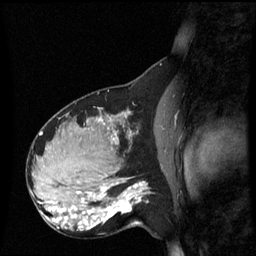
Breast MRI (dynamic contrast-enhanced), one sagittal slice. Position 34 of 60 along the scan axis. Dynamic contrast-enhanced series, image 2 of 3 at this slice position (ordered by acquisition). 1.5 T. TE 4.2 ms, TR 8.9 ms. 2.2 mm slice thickness. 256 × 256 image matrix, field of view 220 × 220 mm. Patient: female, 31 years. From the clinical record (not read from this slice): setting: breast cancer imaged before/during neoadjuvant chemotherapy; receptor status: HR-positive, HER2-negative.
Structures marked on this image (semi-automatically segmented with operator editing):
- analysis volume of interest (the breast-tissue region the enhancement analysis was run in; not a lesion): bounding box (x1, y1, x2, y2) in pixels: (90, 180, 151, 229)
- tumour enhancement mask (voxels above the 70 % enhancement threshold inside the analysis volume of interest): (90, 182, 147, 229)